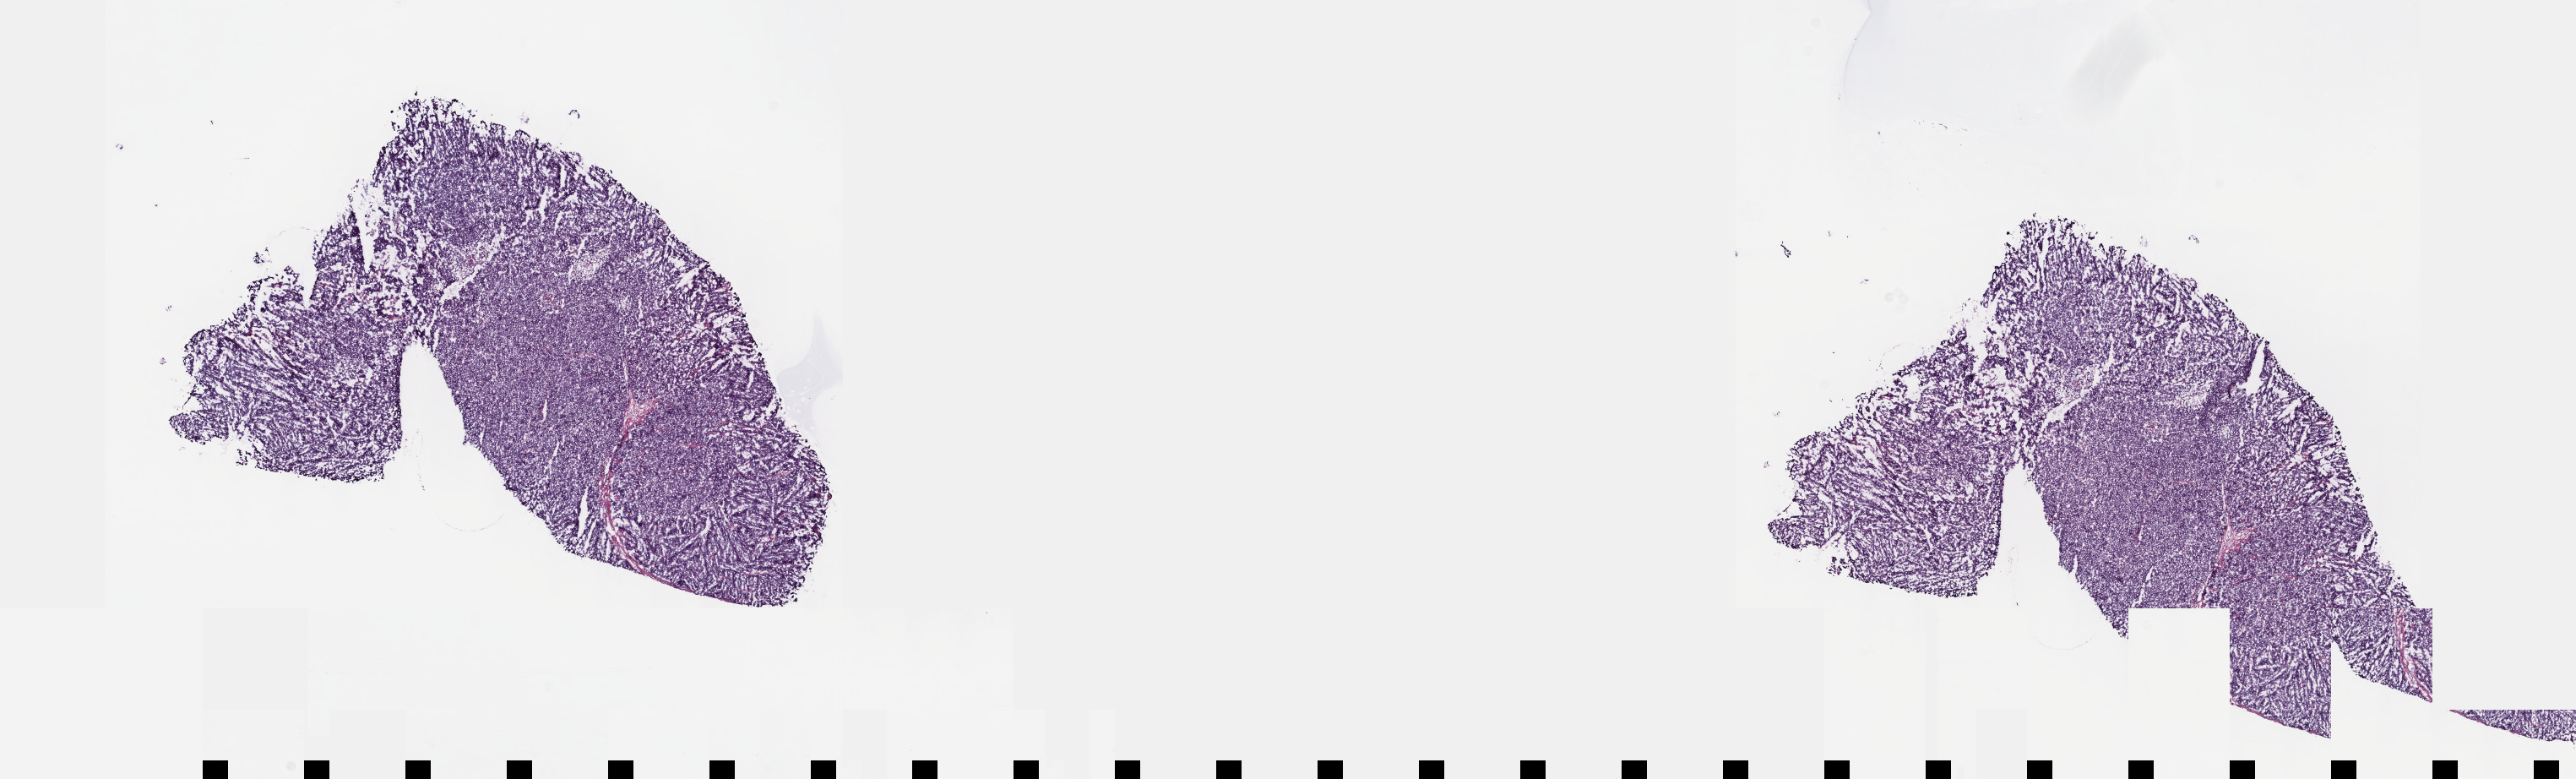
Whole-slide histology image, H&E, whole scanned area (about 24.6 x 7.5 mm, acquisition: 40x scan) shown as a low-resolution overview. Frozen section from the top of the tissue portion. Bladder, primary tumour sample. Female patient; age at initial diagnosis 67 years. Histologic grade: high grade. Composition of this section per pathologist review: tumour cells 85%, tumour nuclei 90%, normal cells 0%, stromal cells 15%, necrosis 0%. Inflammatory infiltration, as recorded: lymphocyte infiltration 0%, monocyte infiltration 0%, neutrophil infiltration 0%.
AJCC pathologic stage: III (7th edition). TNM: T3b NX M0. Pathologic diagnosis: Transitional cell carcinoma (posterior wall of bladder).